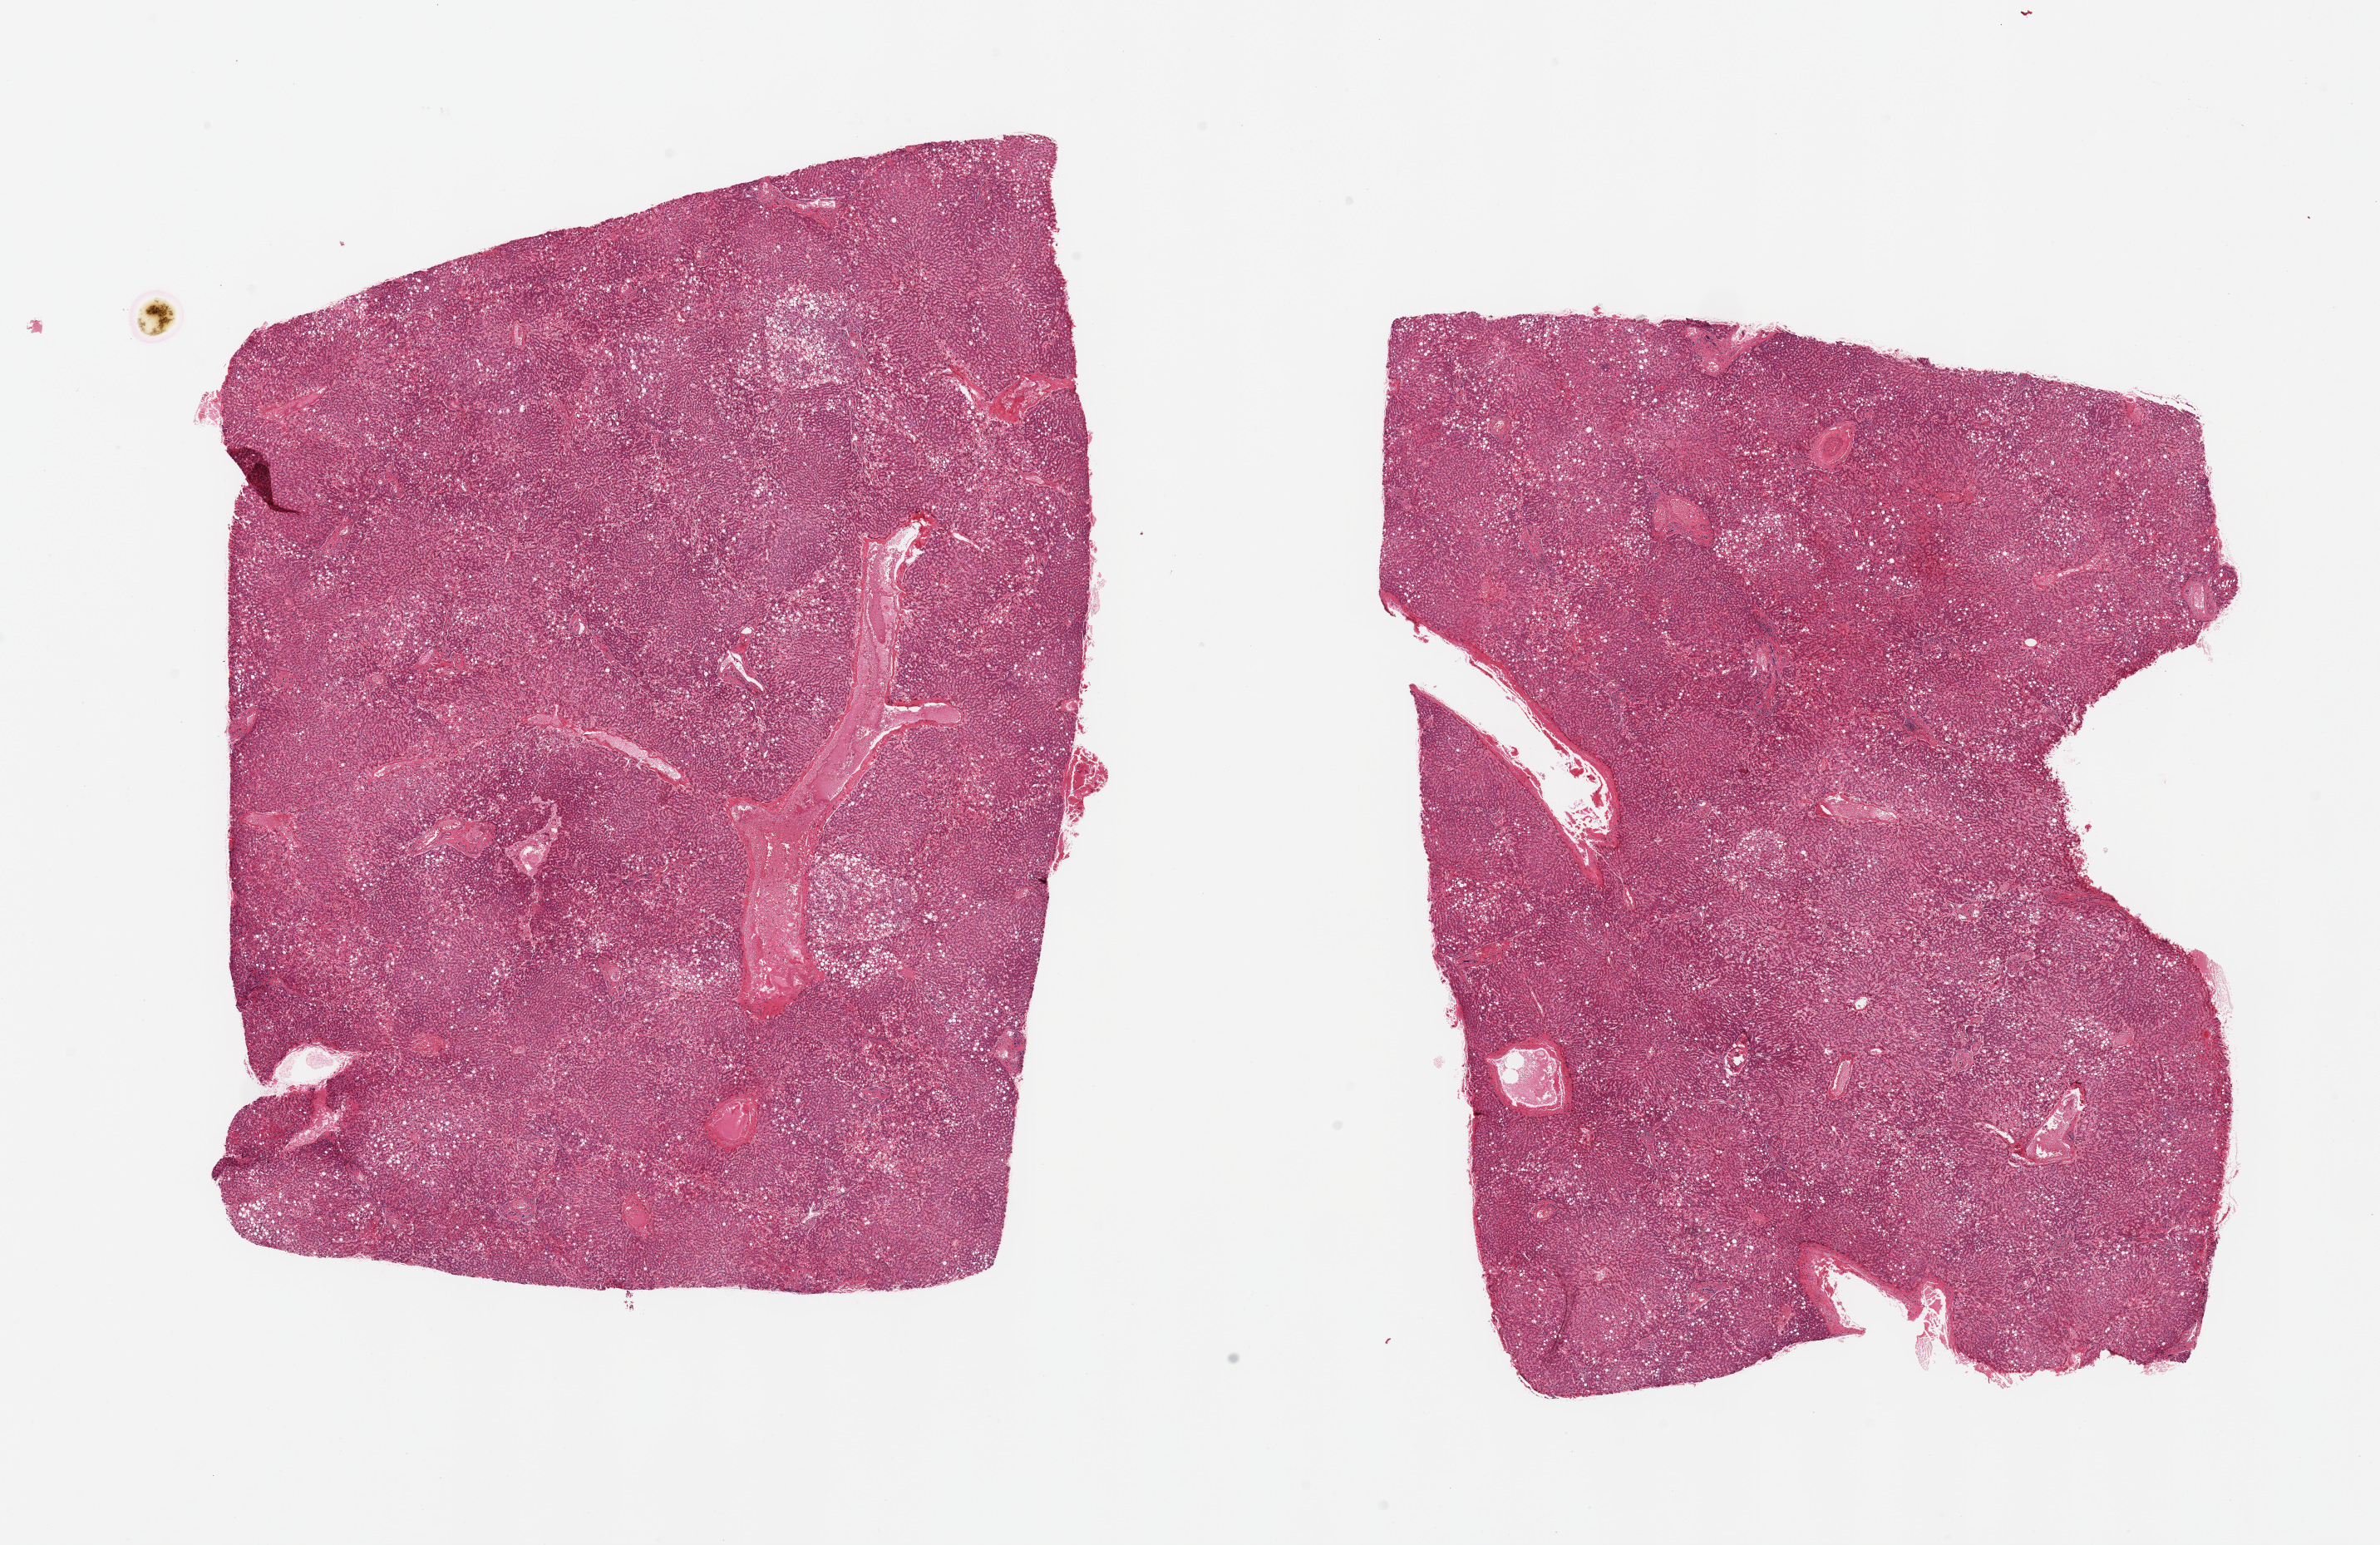
Whole-slide image, haematoxylin and eosin stain — low-resolution overview of the scanned area, about 22.6 x 14.7 mm, PAXgene-fixed paraffin-embedded (PFPE) section, section of liver (target tissue), tissue donor sample. Donor sex: female.
Reviewer comment on this tissue sample: 2 pieces; moderate macrovesicular steatosis.